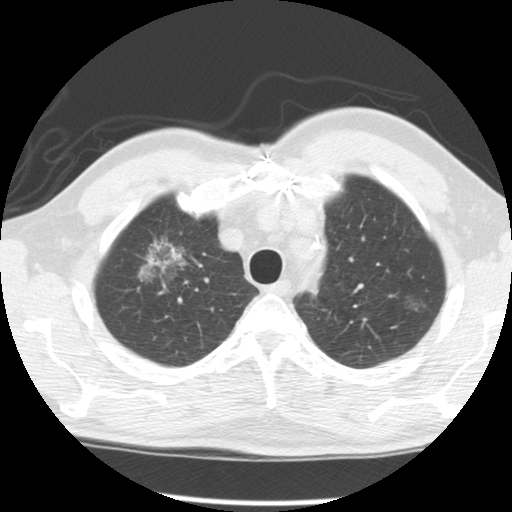
Low-dose screening chest CT, axial slice, second annual screen, lung window (W 1500 / L -600 HU), standard (soft-tissue) reconstruction kernel (STANDARD), 120 kVp. Male participant, aged 64 years at enrolment. Former smoker at enrolment.
• Expert-annotated lung lesion, box from (x=121, y=224) to (x=201, y=298) px.
• The screening reader recorded 2 non-calcified nodules or masses ≥4 mm on this exam (right upper lobe, left upper lobe); which of them this box marks is not recorded.
• Official screen result: positive, other.
• Participant outcome: lung cancer diagnosed 429 days after this screen (after the third annual screen) — adenocarcinoma, NOS, right upper lobe, well differentiated (G1), stage IB (AJCC 6th edition), 45 mm at pathology.